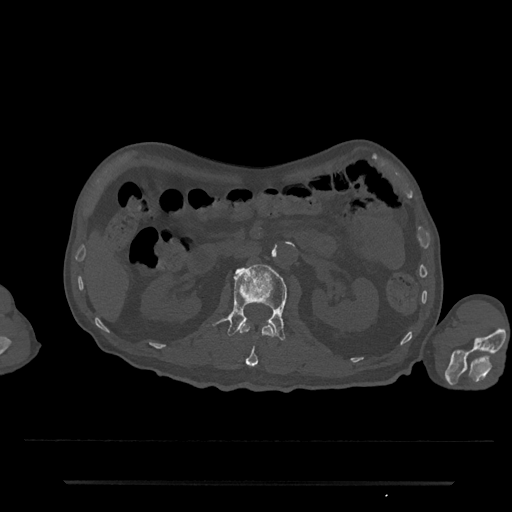
CT including the spine, one axial slice. Slice 86 of 797 in the series (ordered by position). 120 kVp. Bone window (W 1800 / L 400 HU). 0.5 mm slice thickness. 512 × 512 image matrix, field of view 427 × 427 mm. Patient: male, 74 years. Case-level facts recorded for this patient, not image findings: primary cancer: prostate.
Outlined on this slice (semi-automatically segmented with operator editing):
- L1 vertebra: box from (x=239, y=322) to (x=274, y=367) px
- L2 vertebra: (x=227, y=264)–(x=287, y=341)